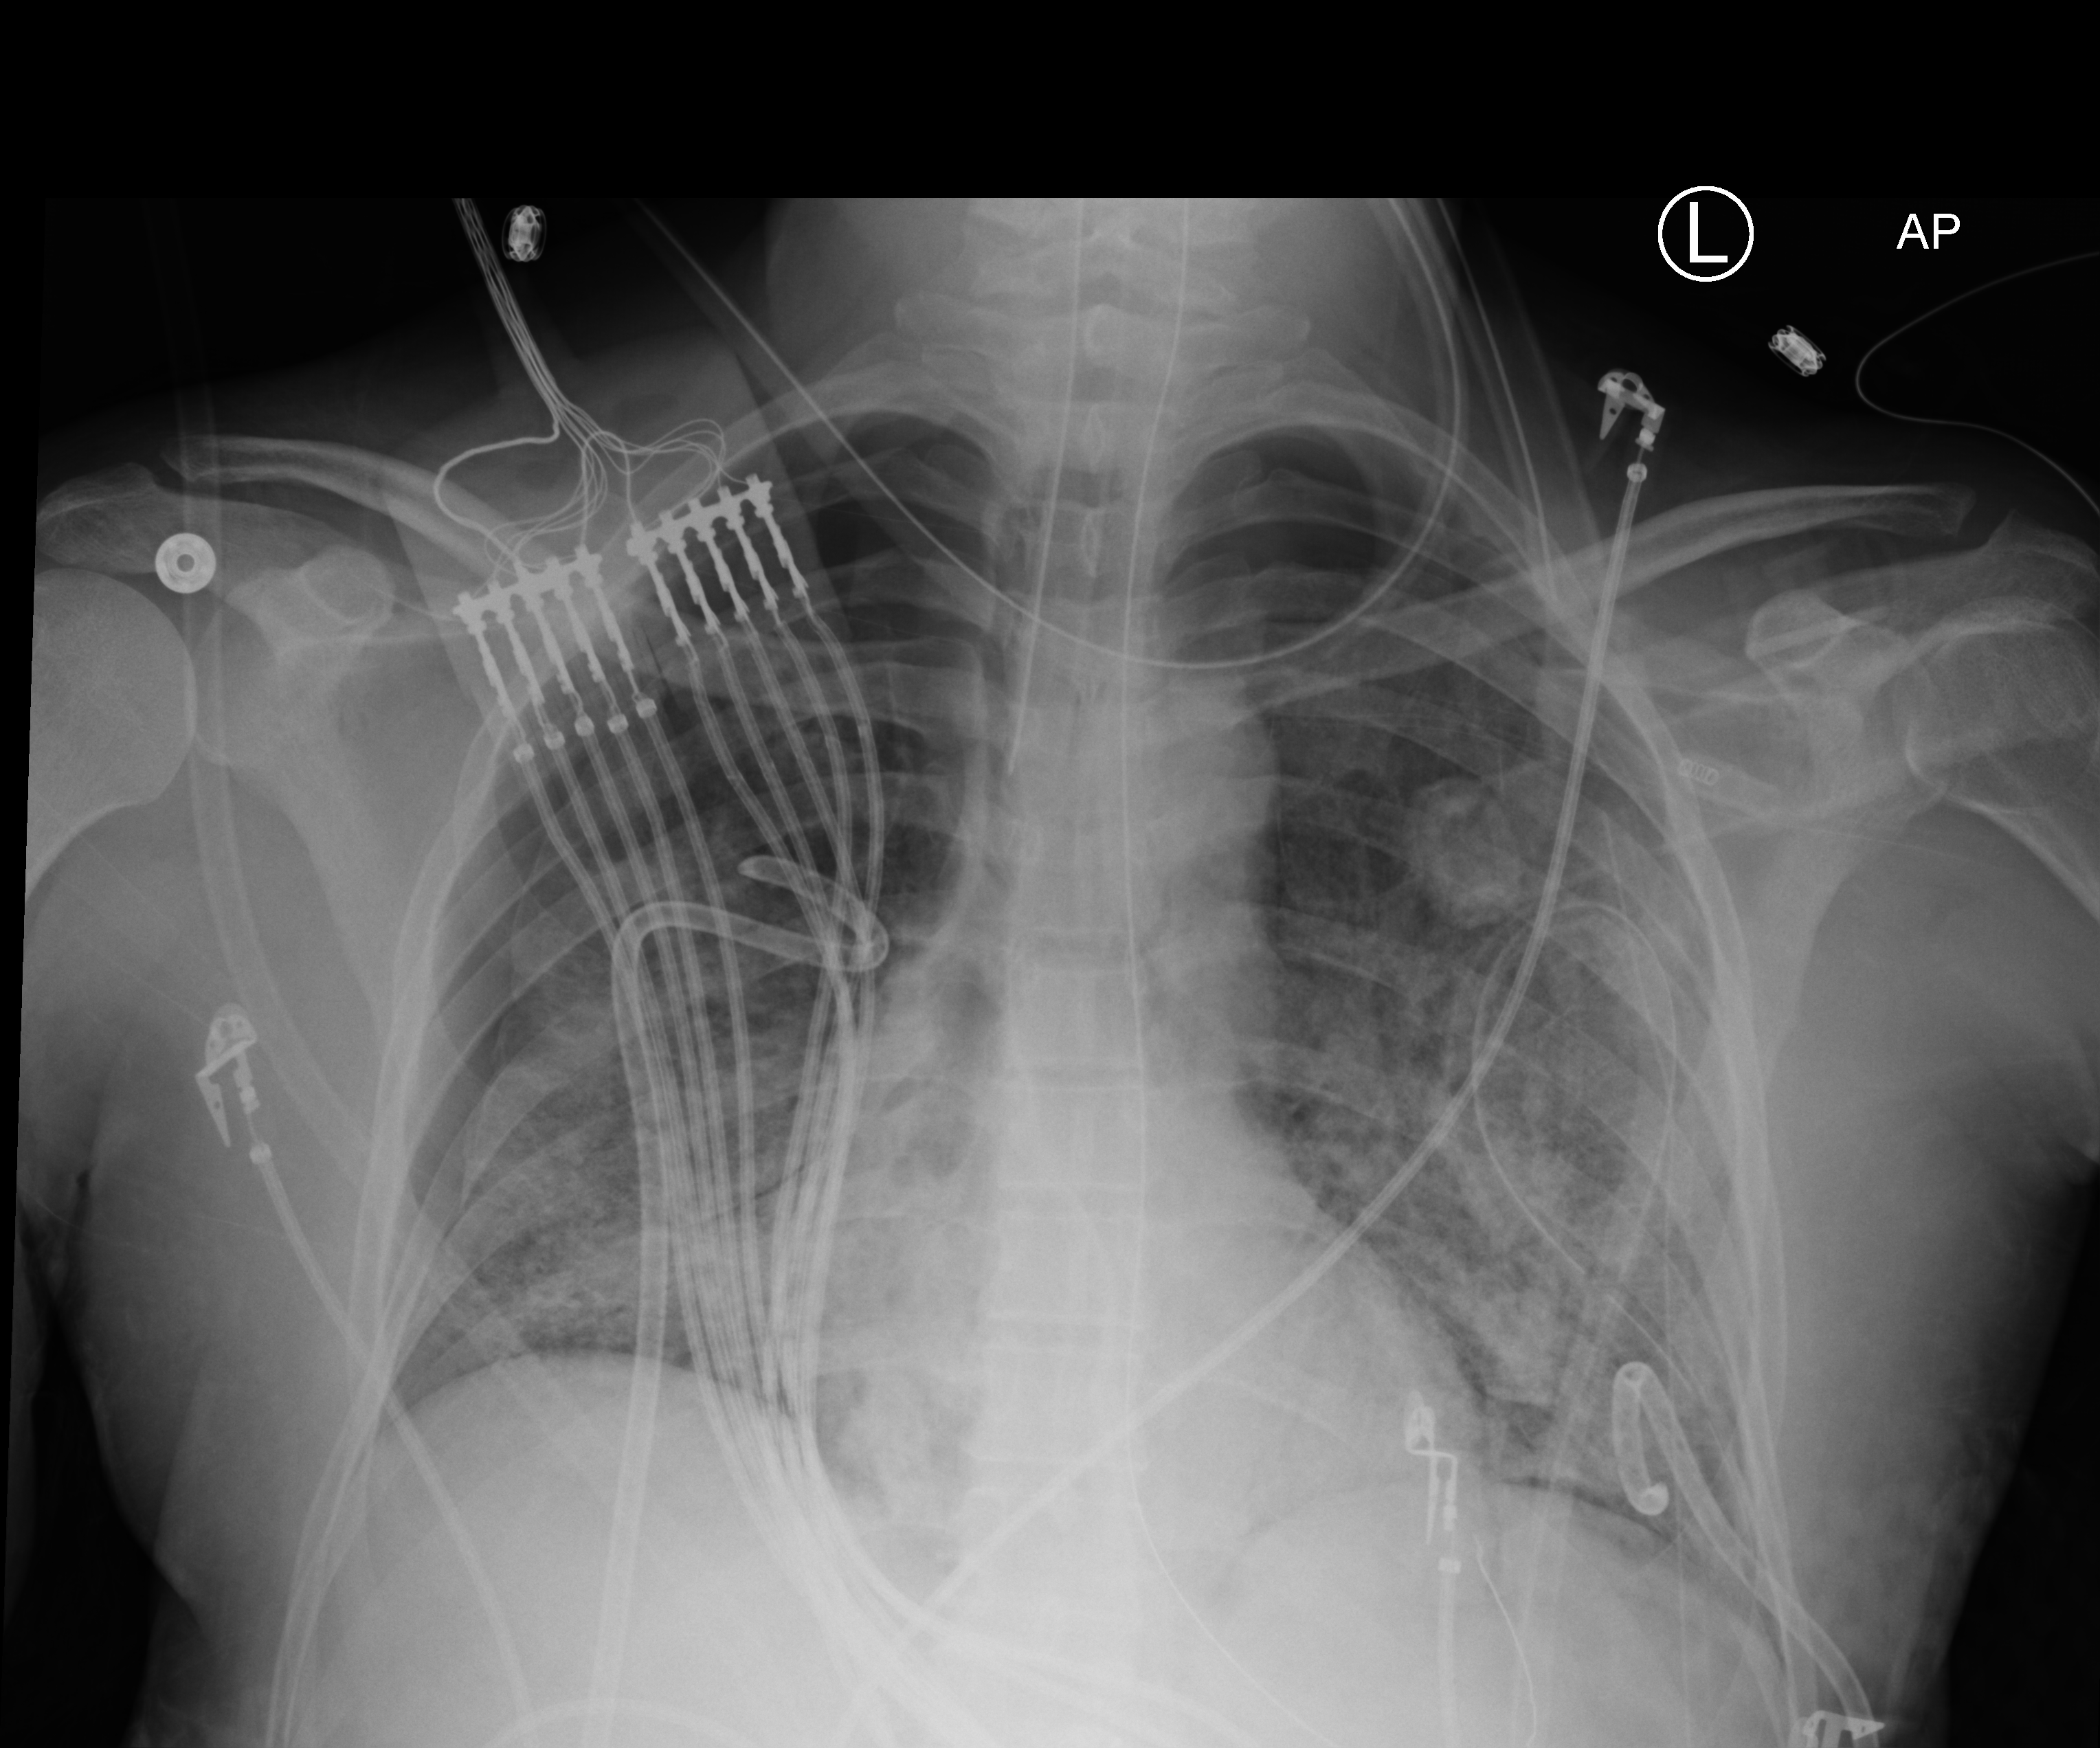
Portable chest radiograph. Adult patient hospitalised with COVID-19, age 18–59 years.
Hospital-stay facts (about this admission, not read from this image; timing relative to this image not recorded):
- smoking status (admission record): never
- length of hospital stay: 41 days
- mechanically ventilated during this hospital stay: yes